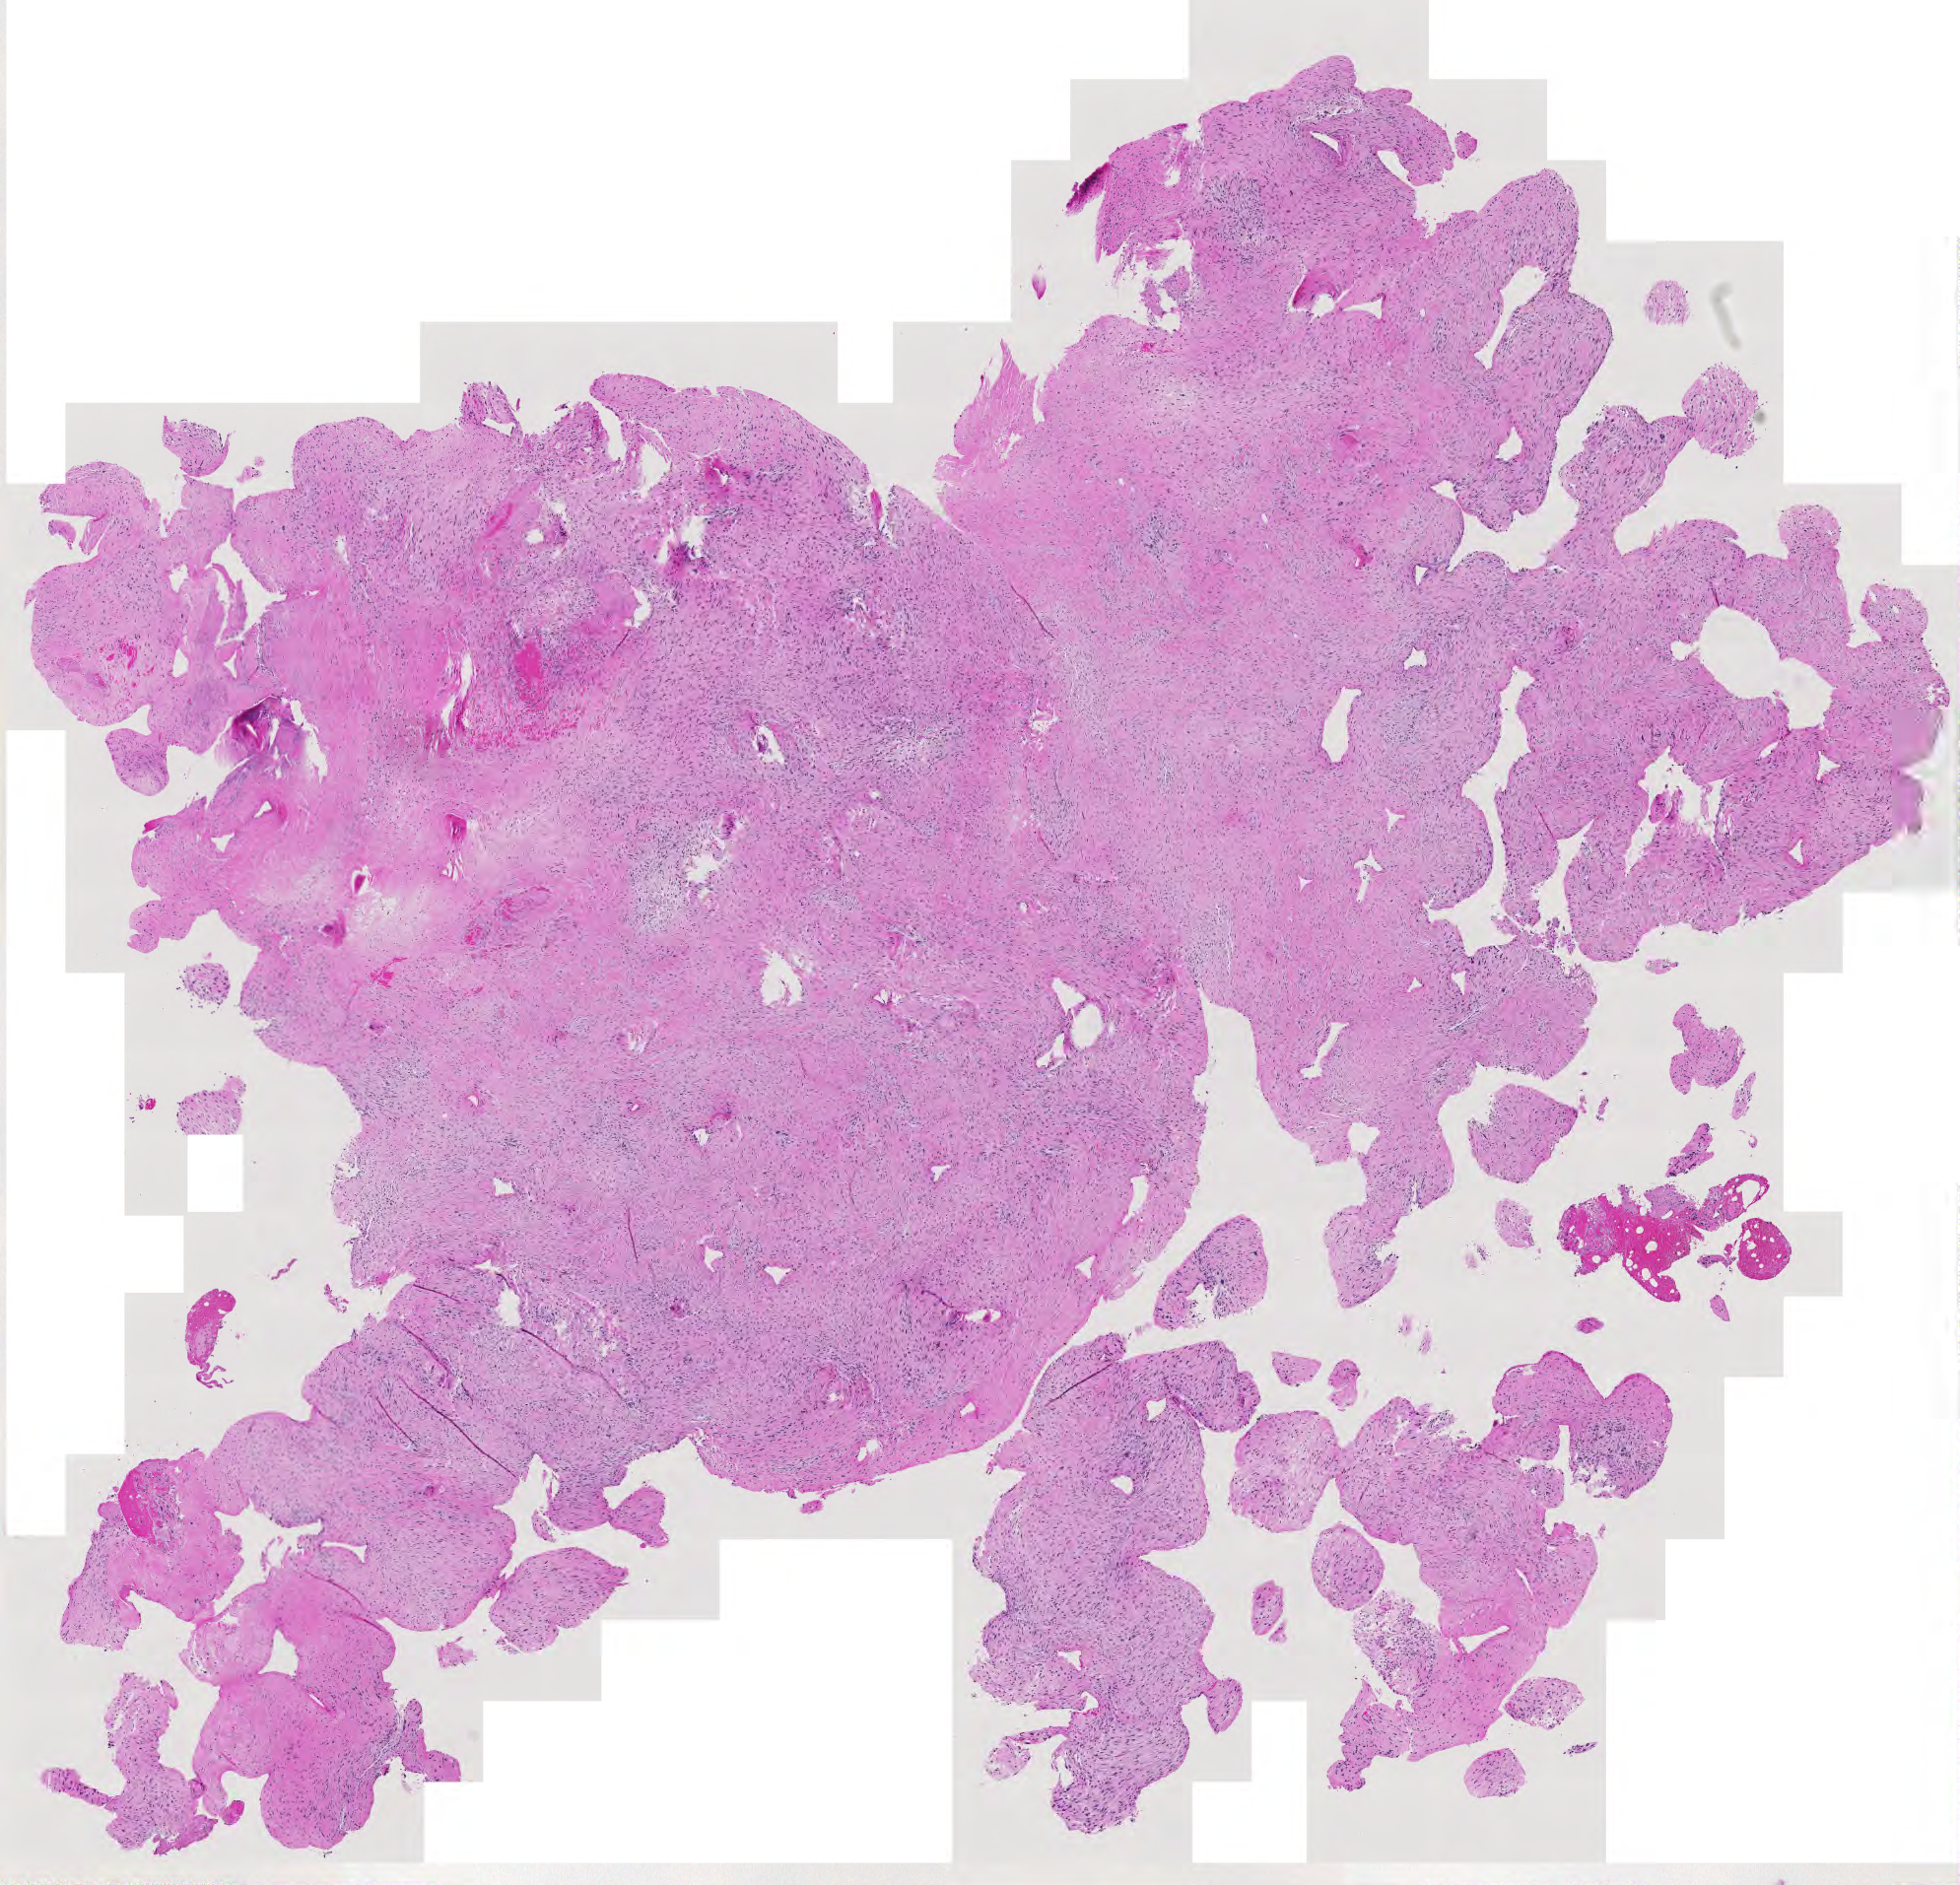
Whole-slide histology image, H&E — a low-resolution overview of the entire scanned area, about 10.3 x 9.9 mm. Tumour tissue sample. Patient: female, age 75 years.
Primary tumour site (as recorded): lower extremity. Patient diagnosis (cohort enrolment): sarcoma (site not recorded at cohort level).